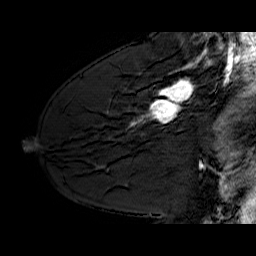
Breast MRI (dynamic contrast-enhanced), one sagittal slice; dynamic contrast-enhanced series, time point 2 of 6 at this slice position (early post-contrast); 1.5 T; TE 6.4 ms, TR 32.9 ms; 4 mm slice thickness; 256 × 256 image matrix, field of view 200 × 200 mm. Female patient. From the clinical record (not read from this slice): setting: breast cancer imaged before/during neoadjuvant chemotherapy; receptor status: HER2-positive.
Outlined on this slice (semi-automatic segmentation, software-assisted and operator-edited):
- analysis volume of interest (the breast-tissue region the enhancement analysis was run in; not a lesion): box from (x=130, y=62) to (x=210, y=128) px
- tumour enhancement mask (voxels above the 100 % enhancement threshold inside the analysis volume of interest): (x=135, y=62)–(x=199, y=123)